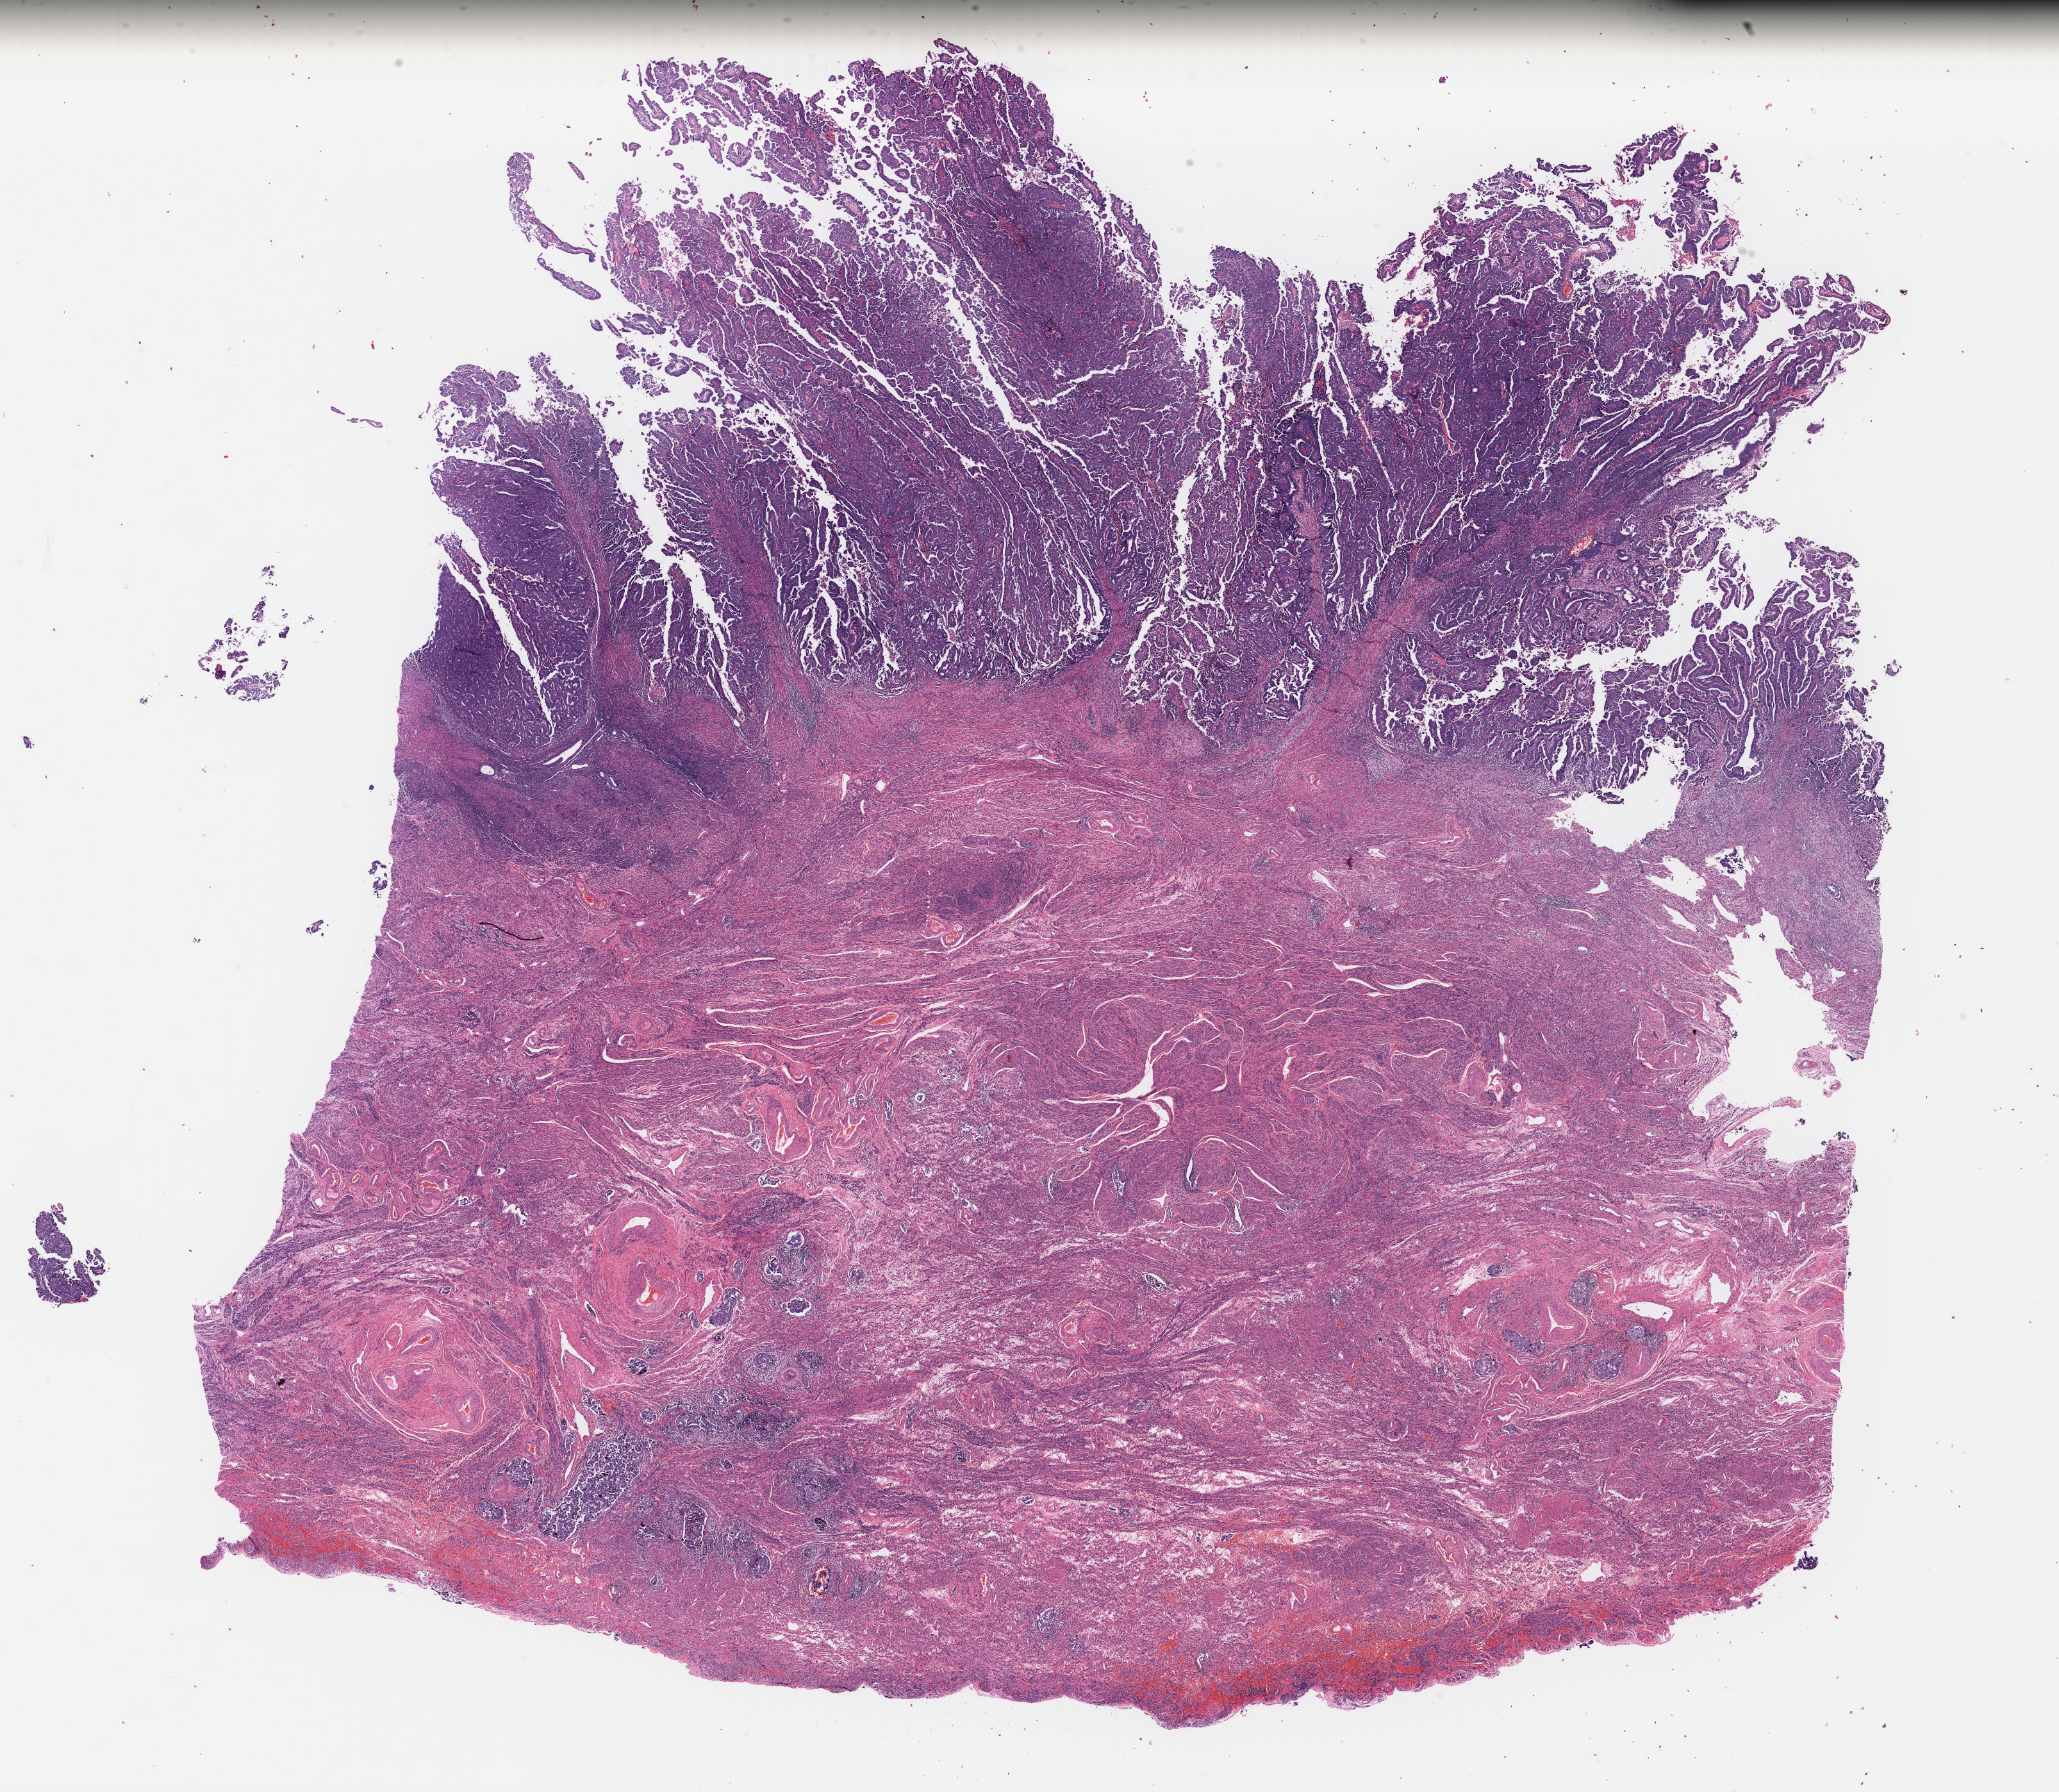
H&E whole-slide image, low-resolution overview of the scanned area, about 25.3 x 22.0 mm (from a 40x scan), FFPE section, primary tumour sample from the uterus. Female, age 71 years at initial diagnosis. Histologic grade: G3 (poorly differentiated).
Diagnosis: Serous cystadenocarcinoma, NOS (endometrium). FIGO stage: IIIC1.